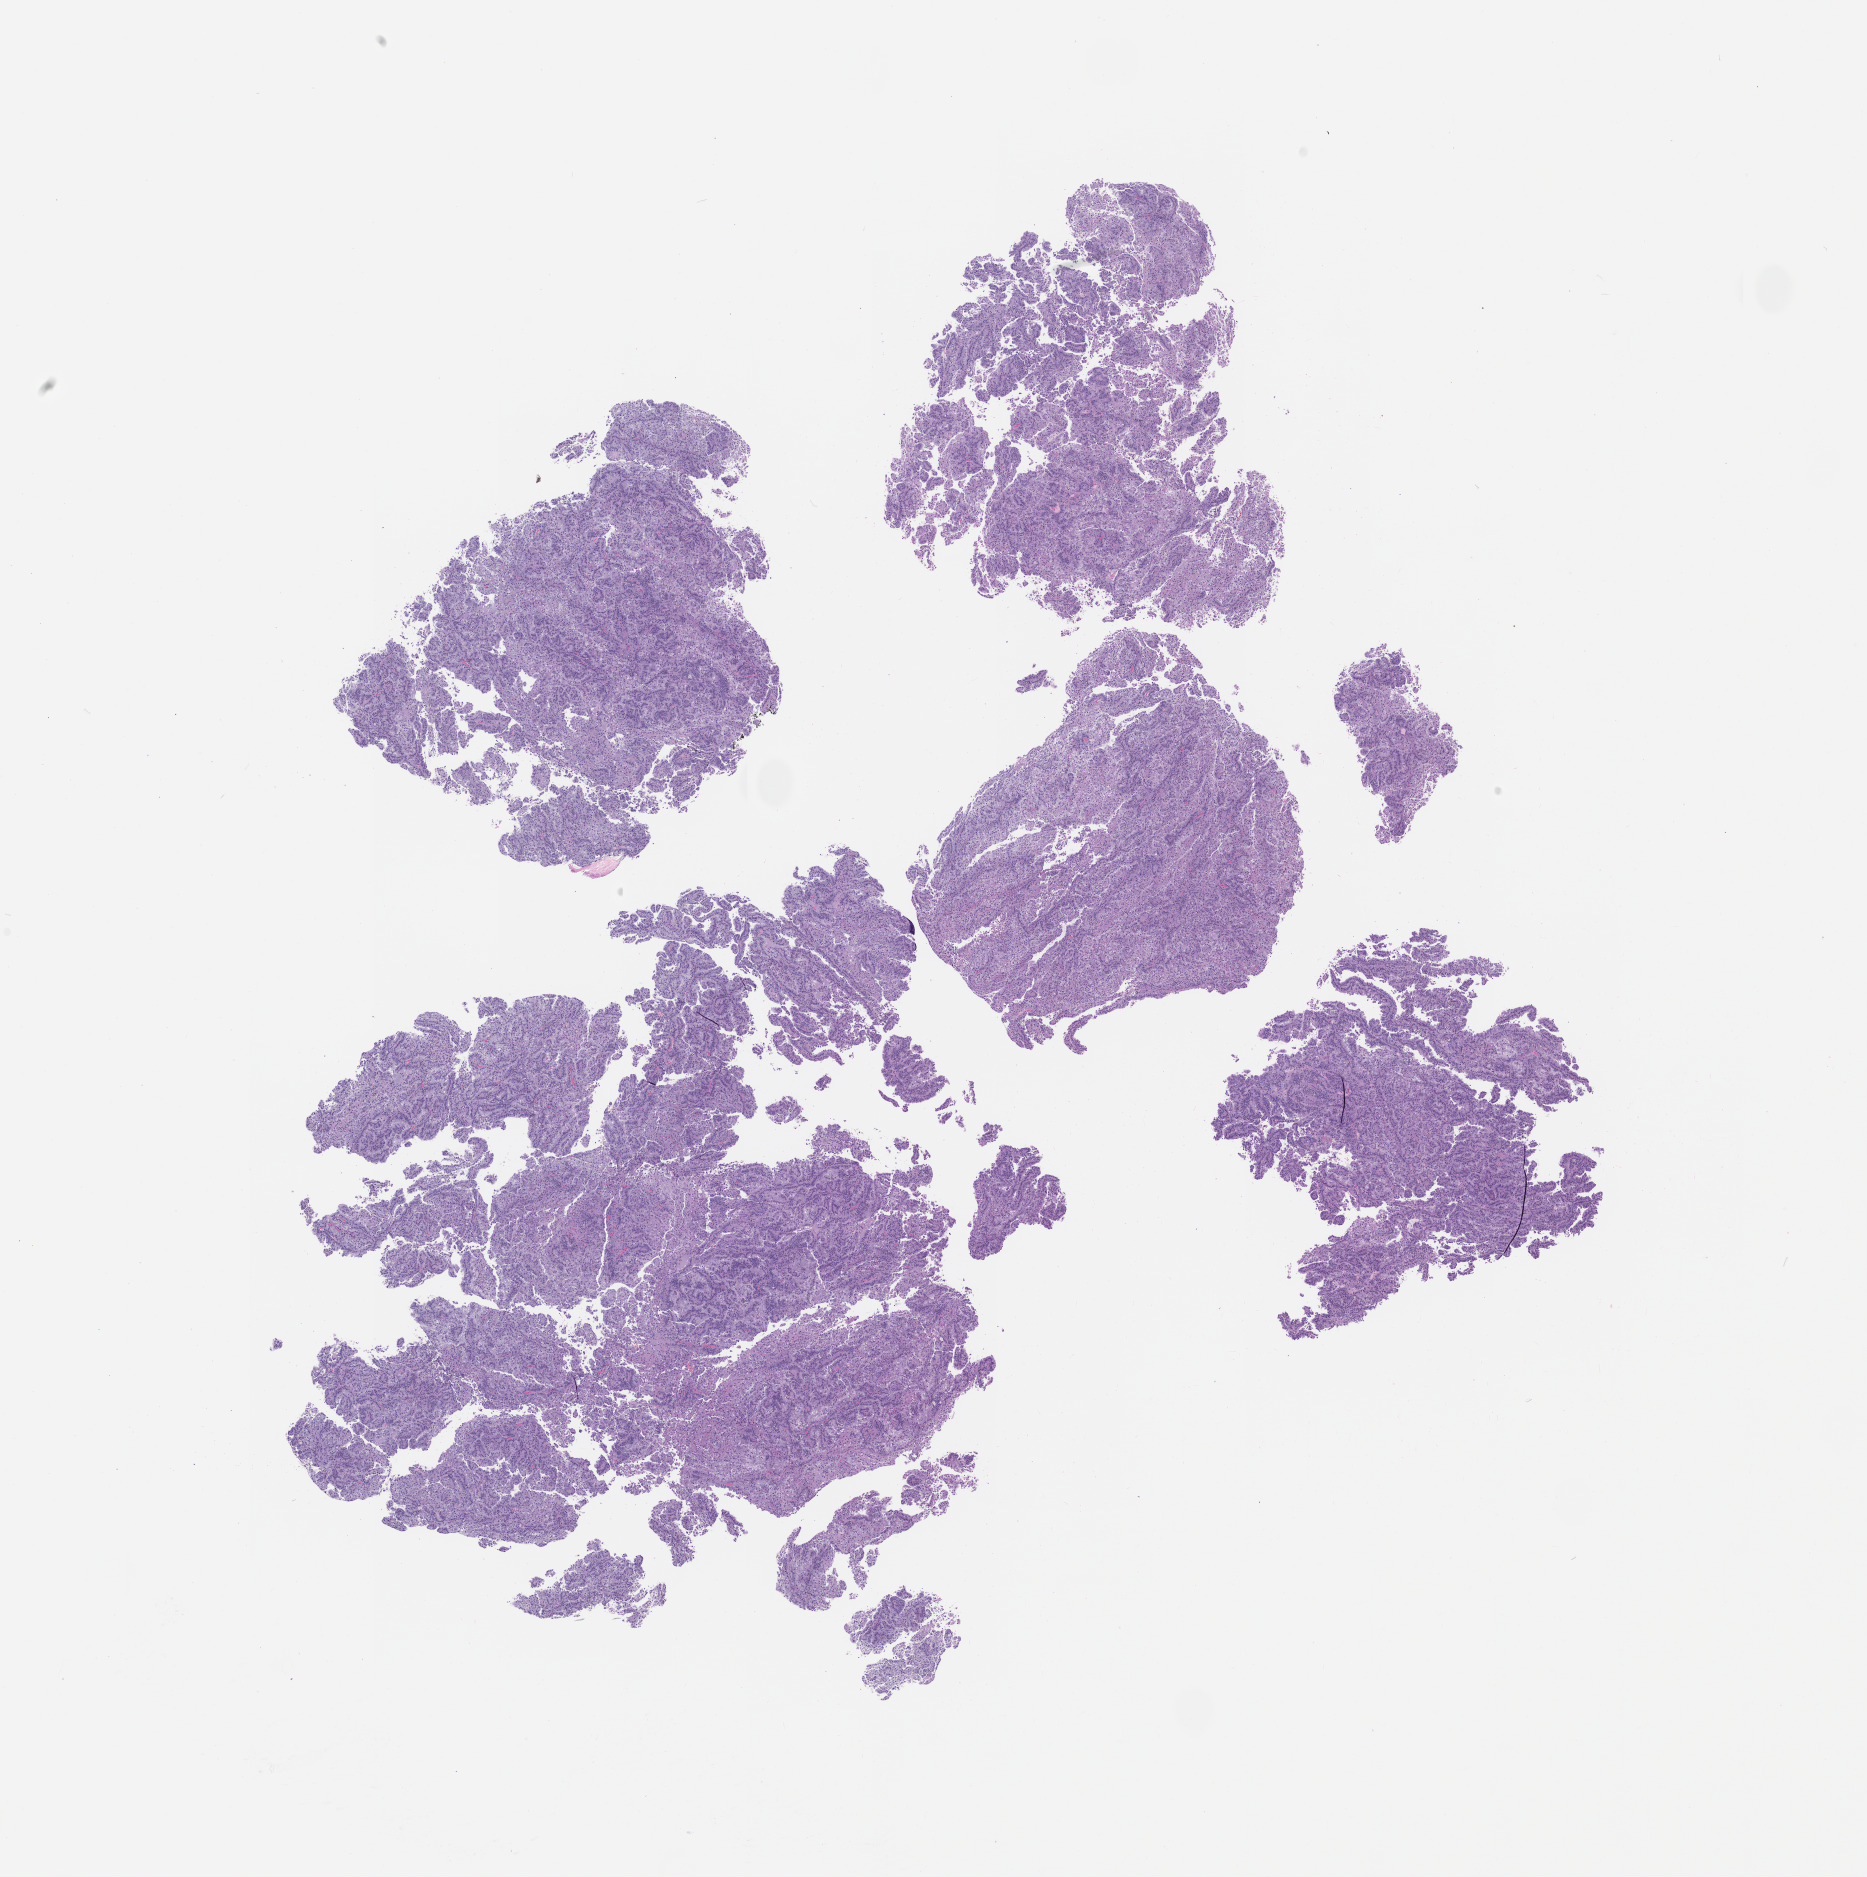
Hematoxylin and eosin (H&E) whole-slide image of a patient-derived xenograft (PDX) tumor grown in a mouse, passage 1 — a low-resolution overview of the entire scanned area, about 15.0 x 15.0 mm, formalin-fixed paraffin-embedded section, originating tumor site category: genitourinary tract.
Originating patient diagnosis: Renal Cell Carcinoma, Not Otherwise Specified.